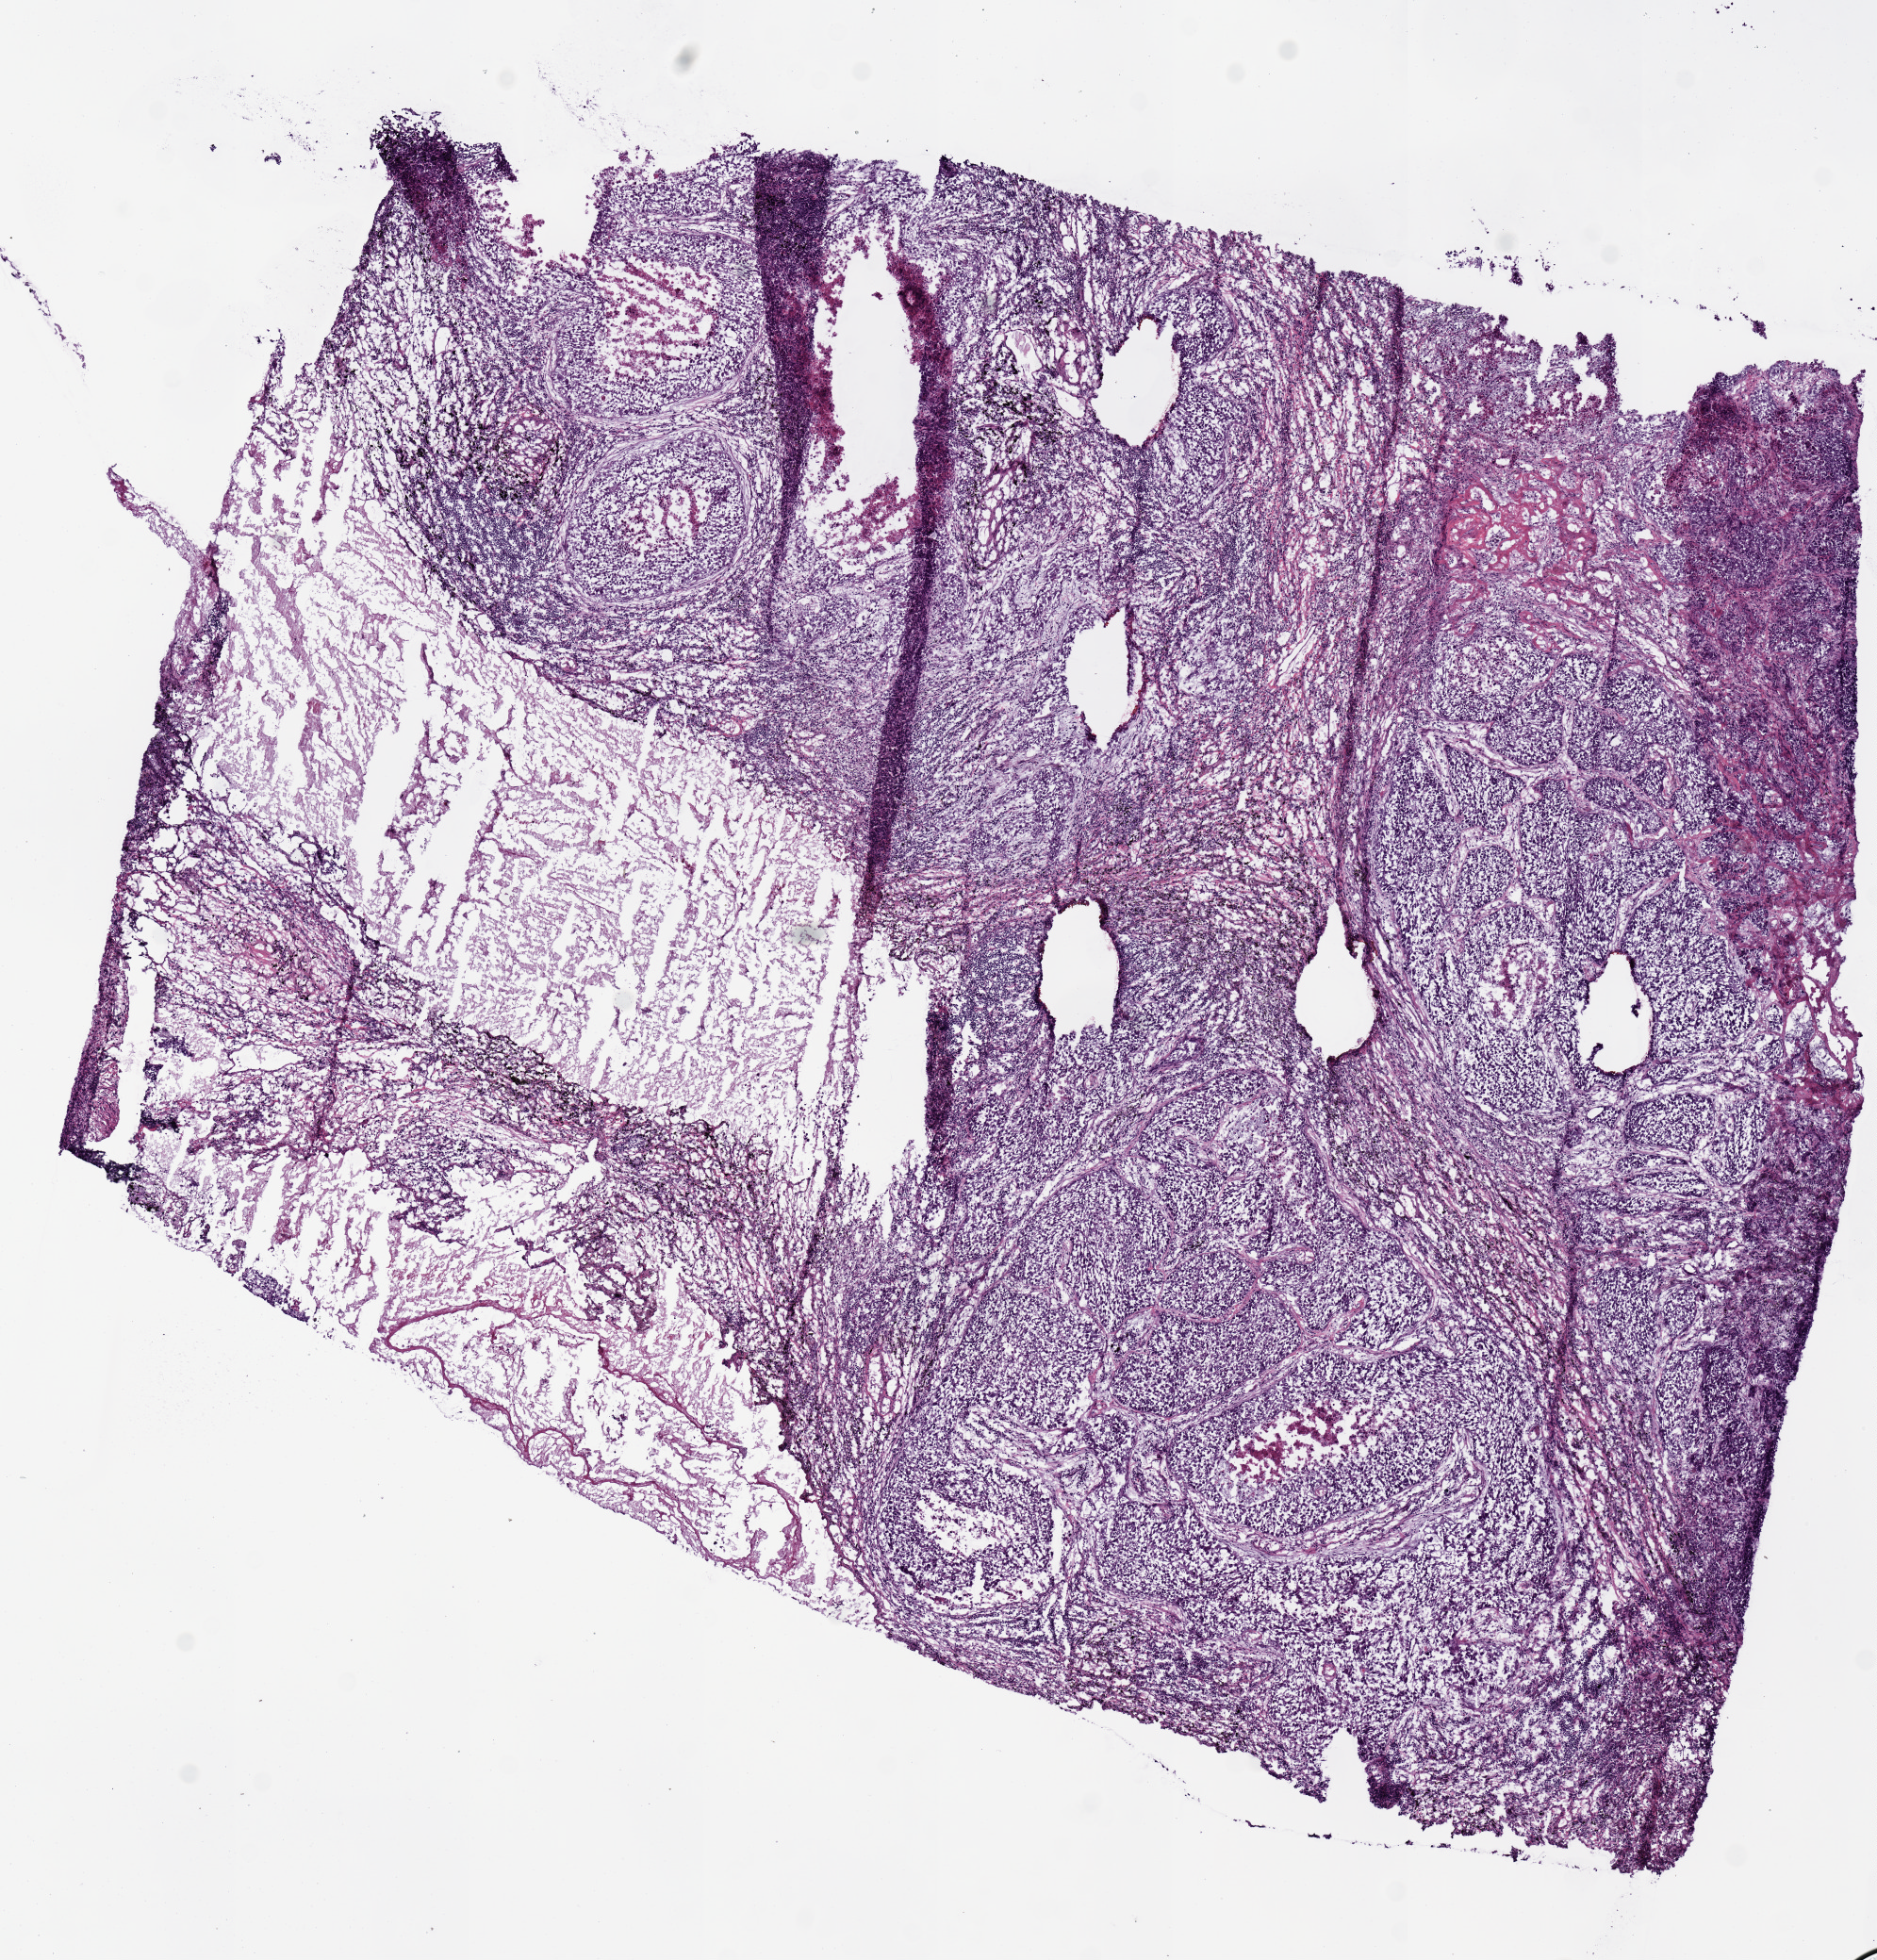
Whole-slide histology image, H&E — a low-resolution overview of the entire scanned area, about 7.9 x 8.2 mm, frozen section, primary tumour sample from the lung. Male, age 52 years at initial diagnosis. Composition of this section per pathologist review: tumour nuclei 75%, necrosis 10%.
- diagnosis: Squamous cell carcinoma, NOS (upper lobe, lung)
- AJCC pathologic stage: IIIA (7th edition)
- laterality: left
- TNM: T2b N2 MX